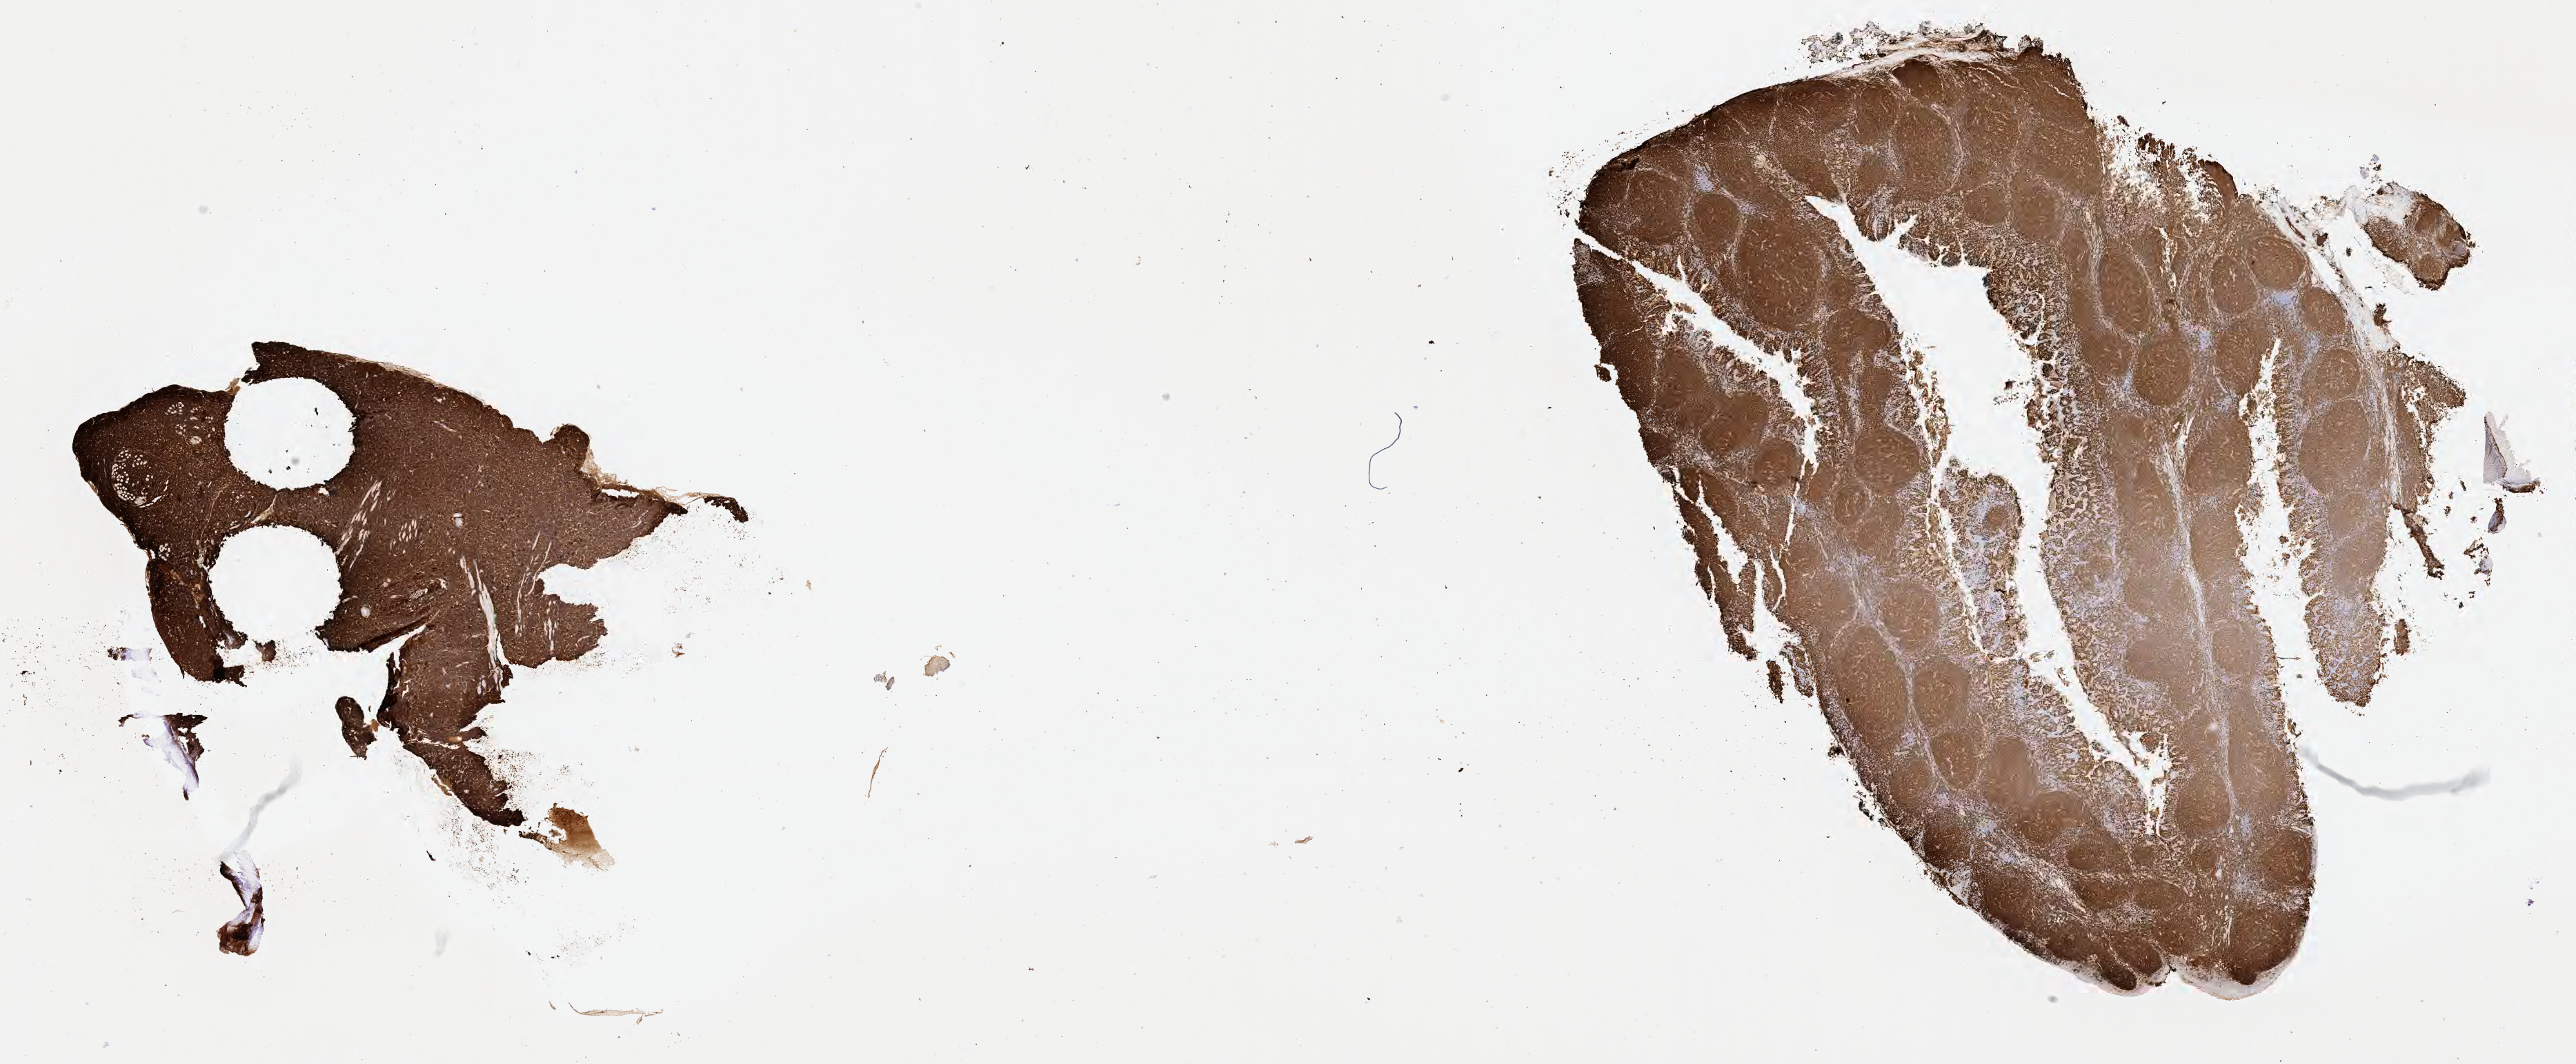
Whole-slide image, immunohistochemical stain for CD20, low-resolution overview of the scanned area, about 30.2 x 12.5 mm. Tumor tissue. Anatomic site: cranium. Male, age 6 years at initial diagnosis.
* diagnosis: Burkitt lymphoma, NOS